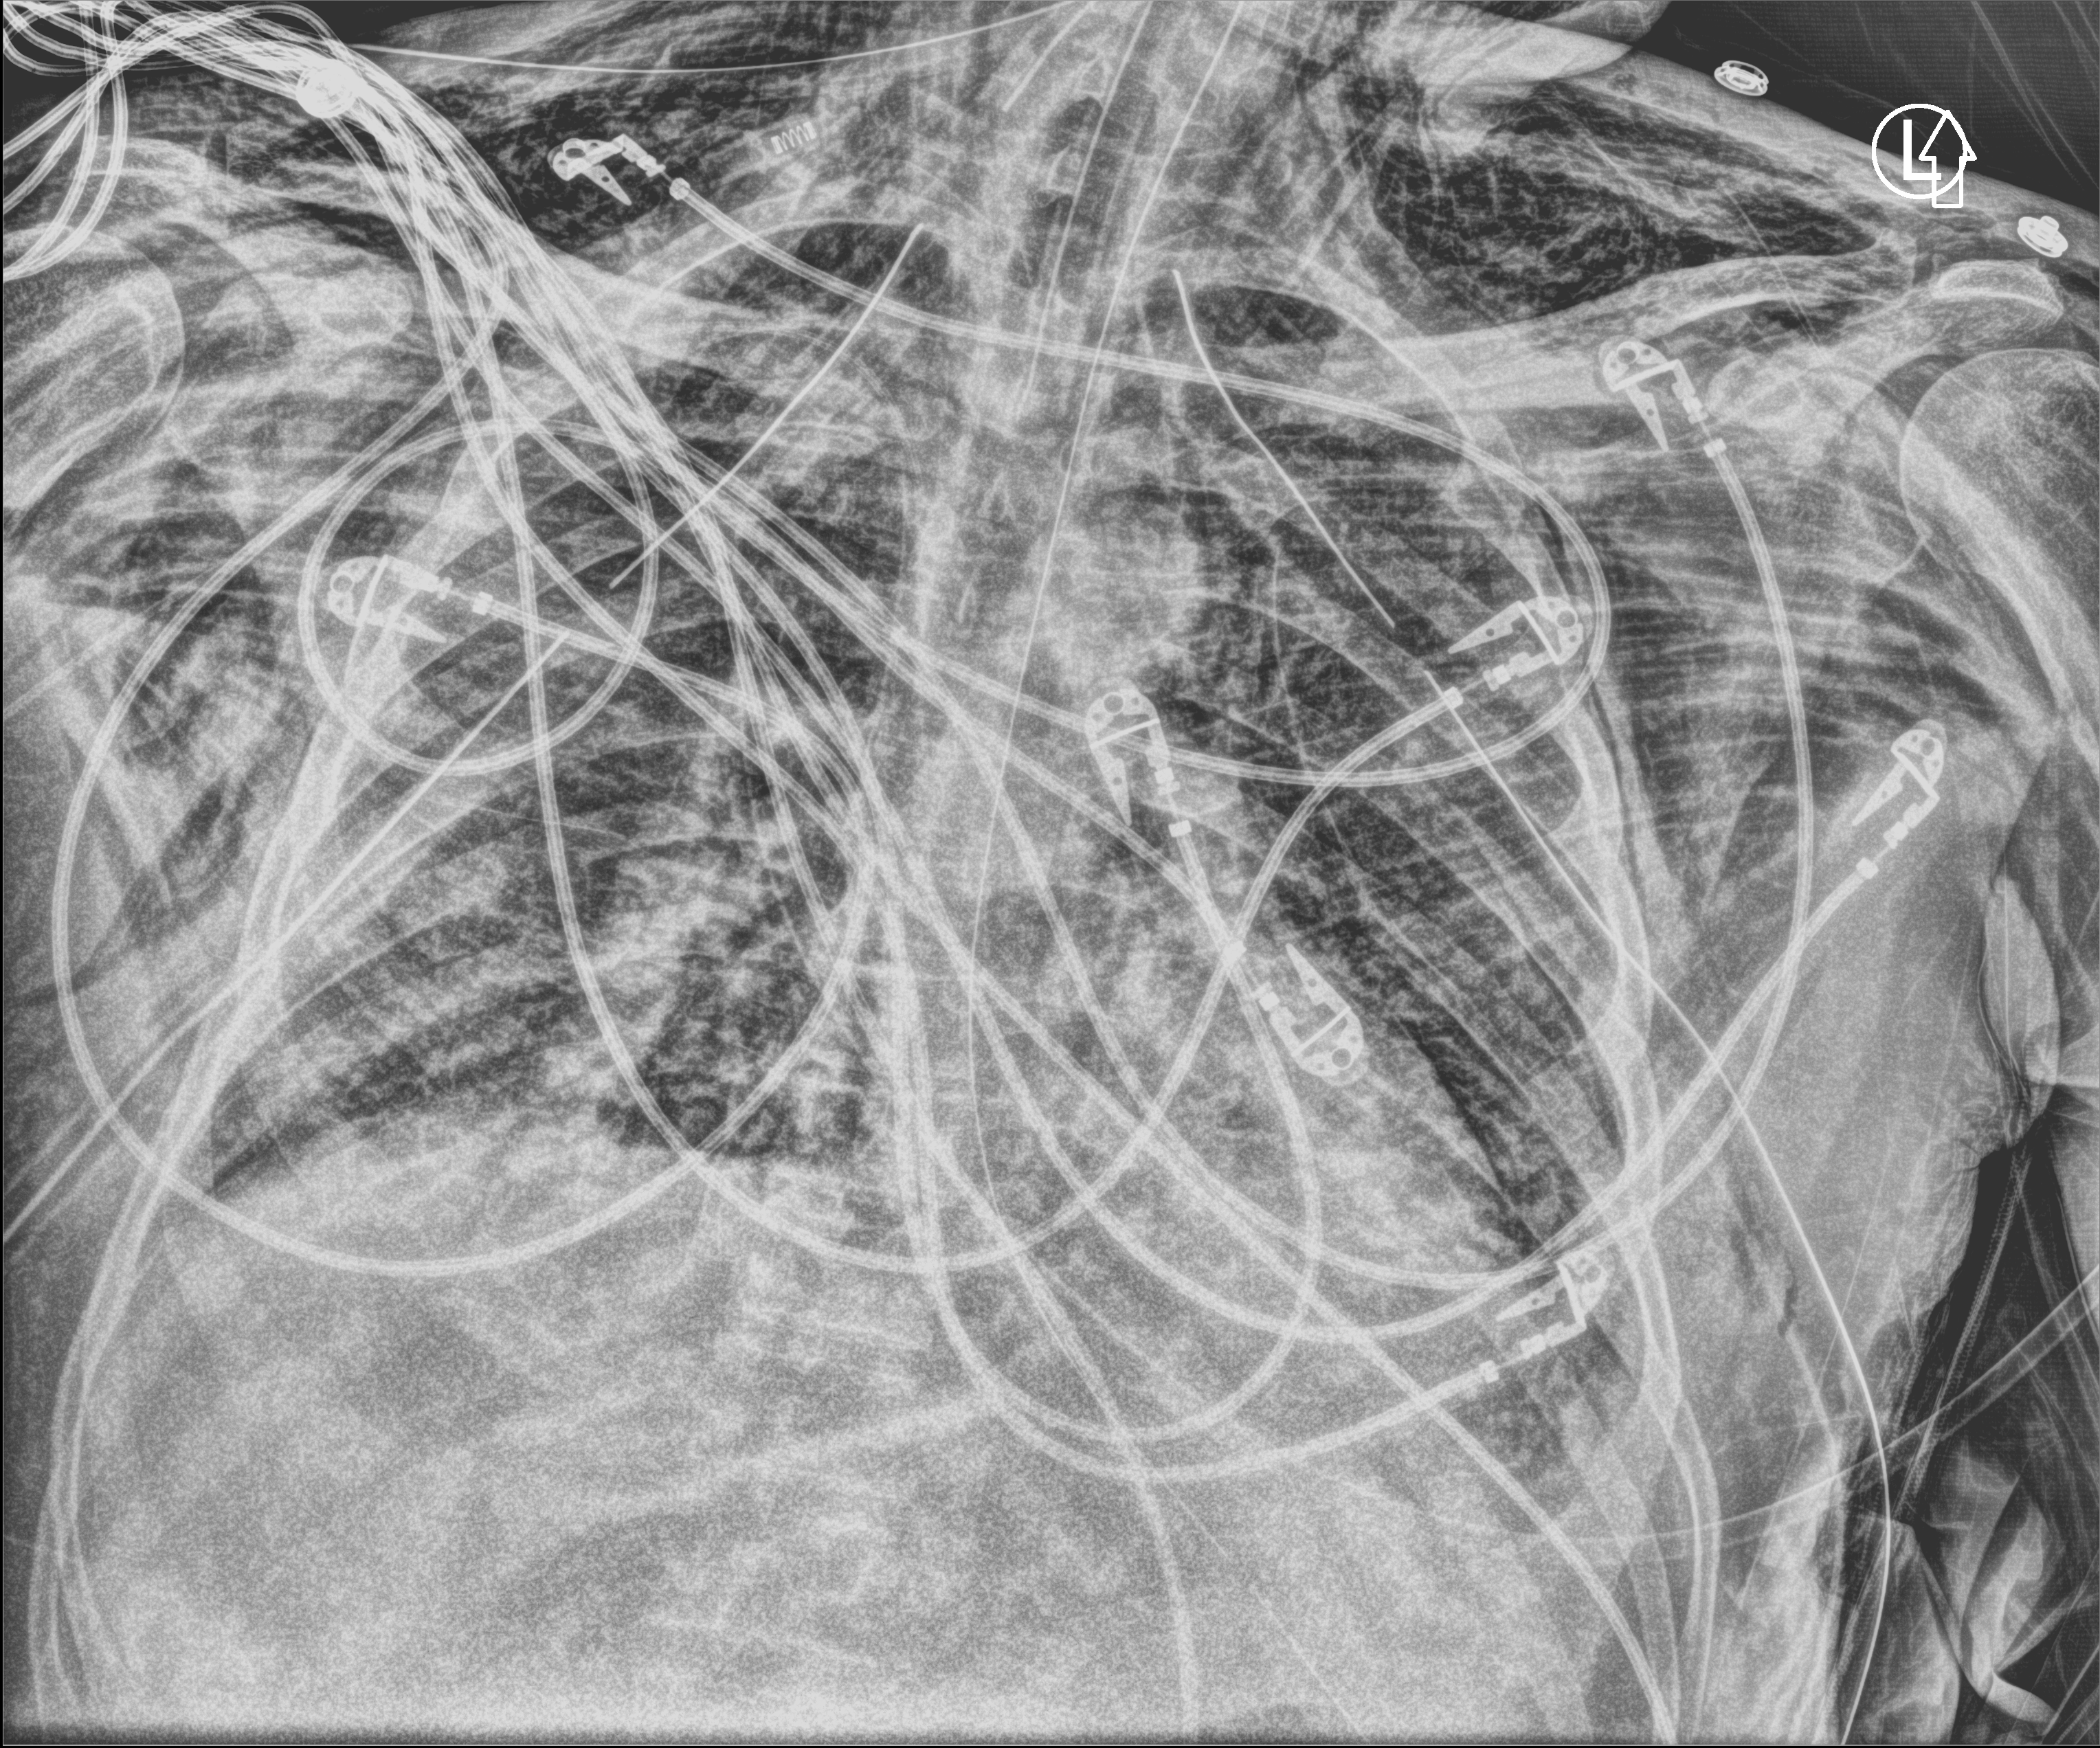
Bedside chest radiograph (computed radiography), anteroposterior (AP) projection. Male patient hospitalised with COVID-19, age 18–59 years.
Admission-level facts for this patient (not findings on this image; timing relative to this image not recorded): mechanically ventilated during this hospital stay: yes; admitted to intensive care during this hospital stay: yes.